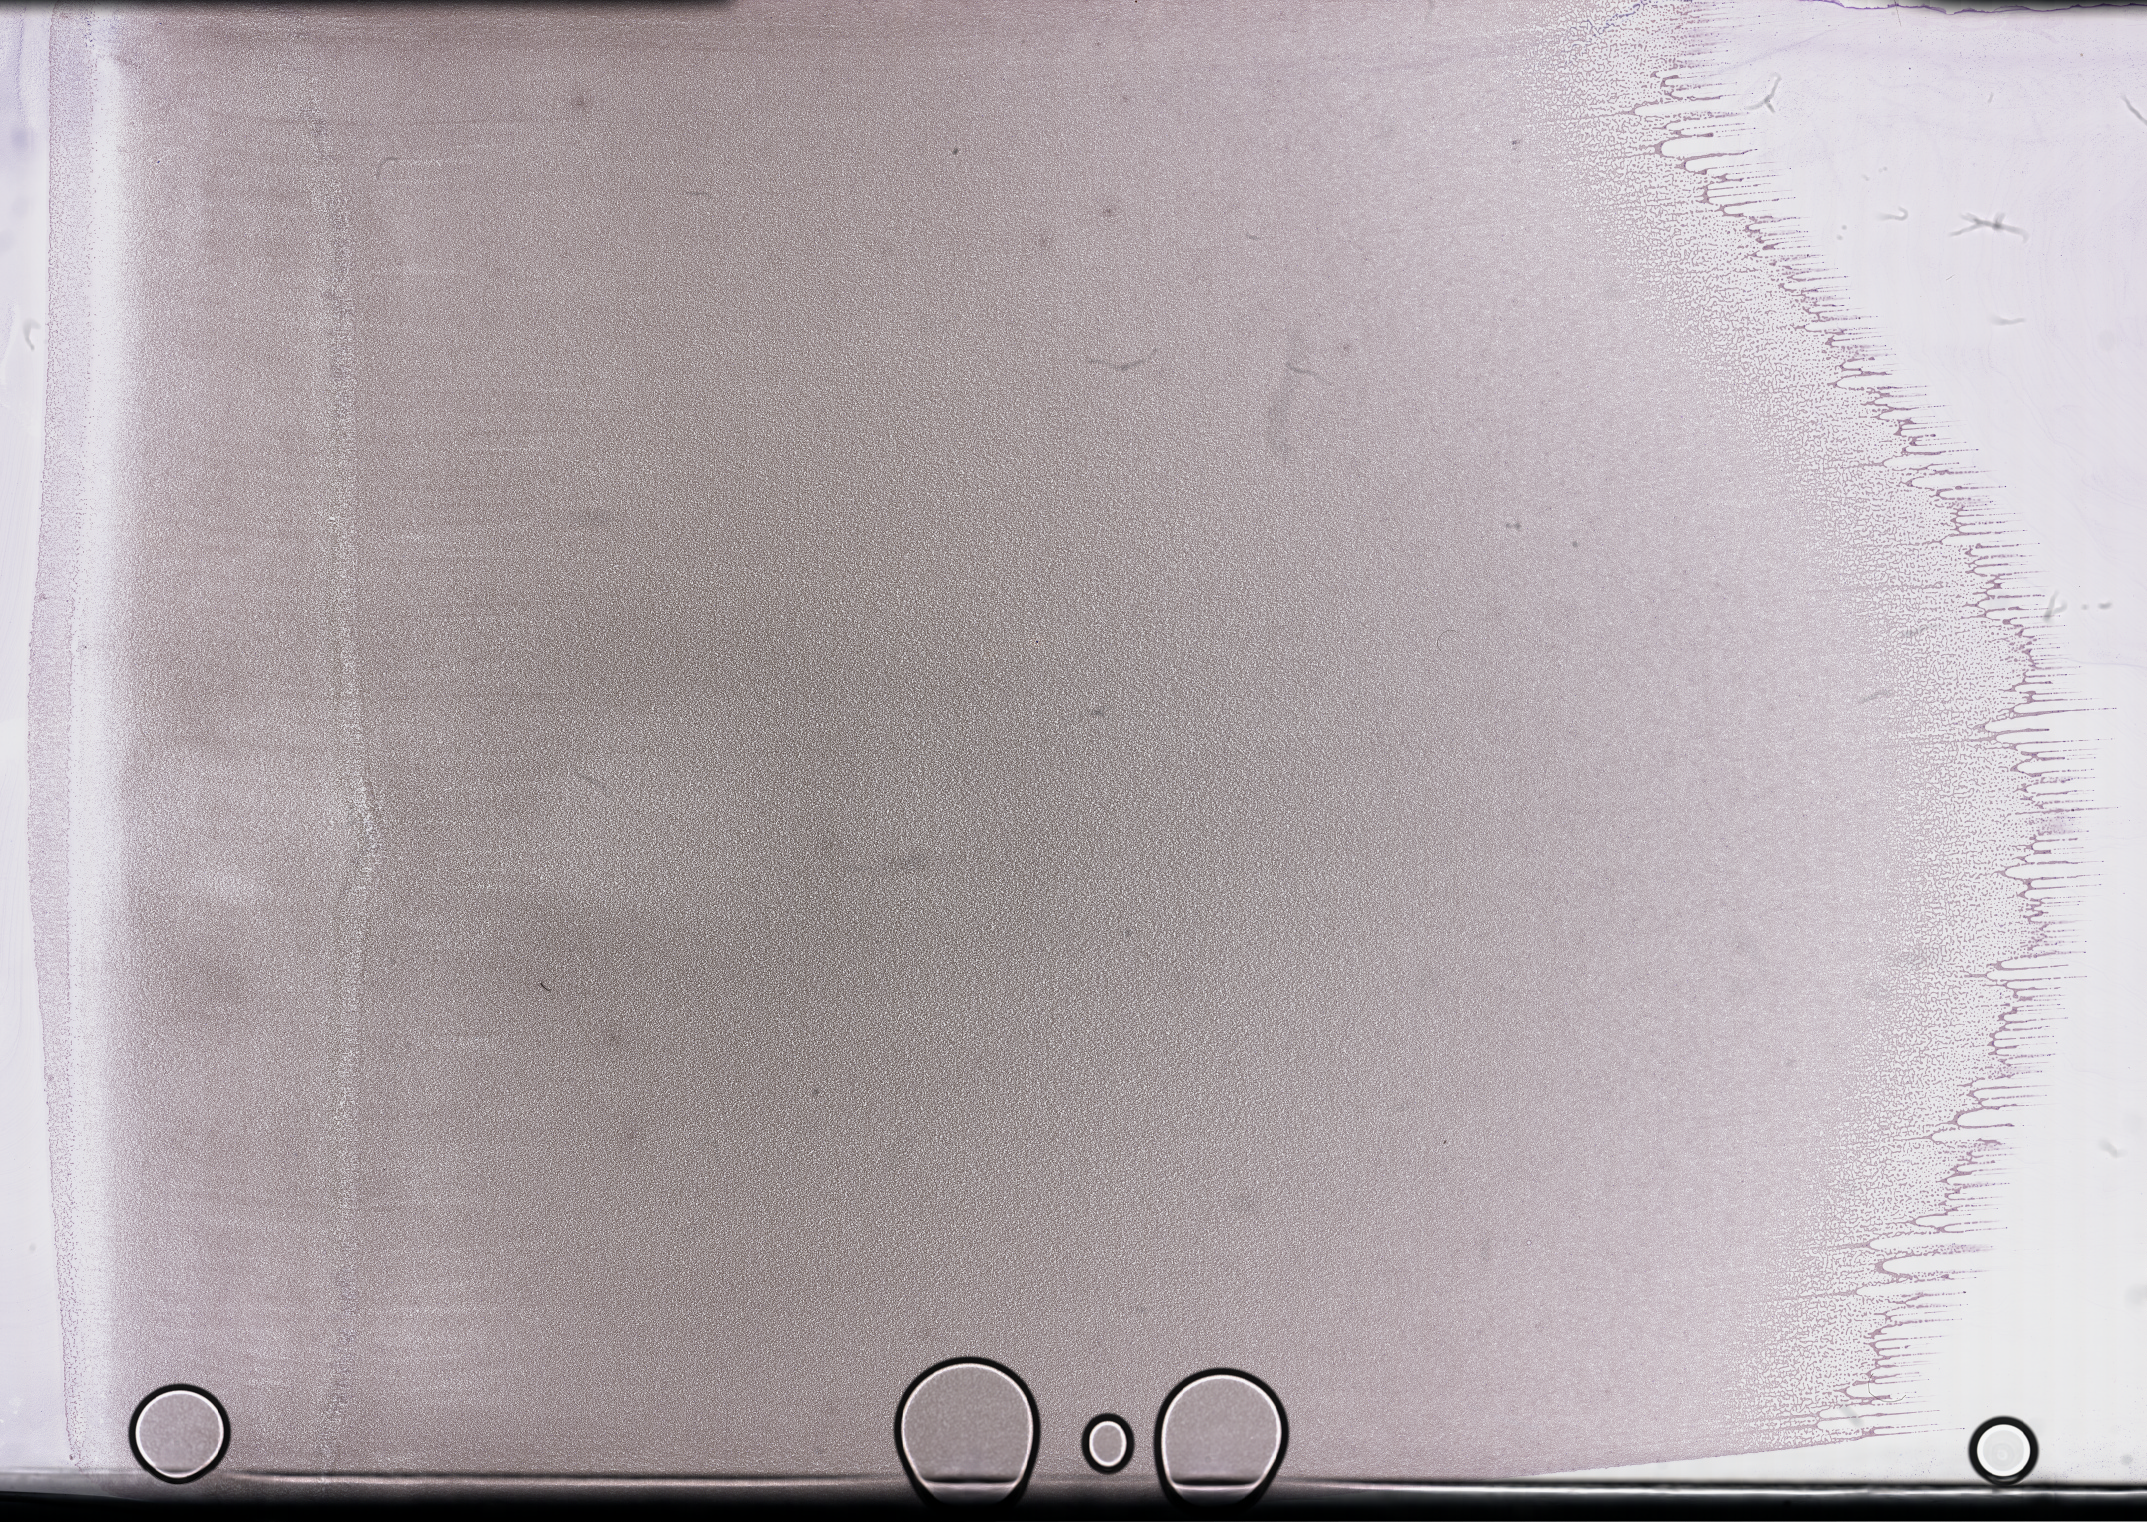
Wright-Giemsa-stained whole blood smear, whole-slide image — low-resolution overview of the scanned area, about 34.7 x 24.6 mm. Smear from an EDTA sample. Specimen time point: collected on treatment. Patient: male.
Patient diagnosis: Plasma Cell Myeloma.